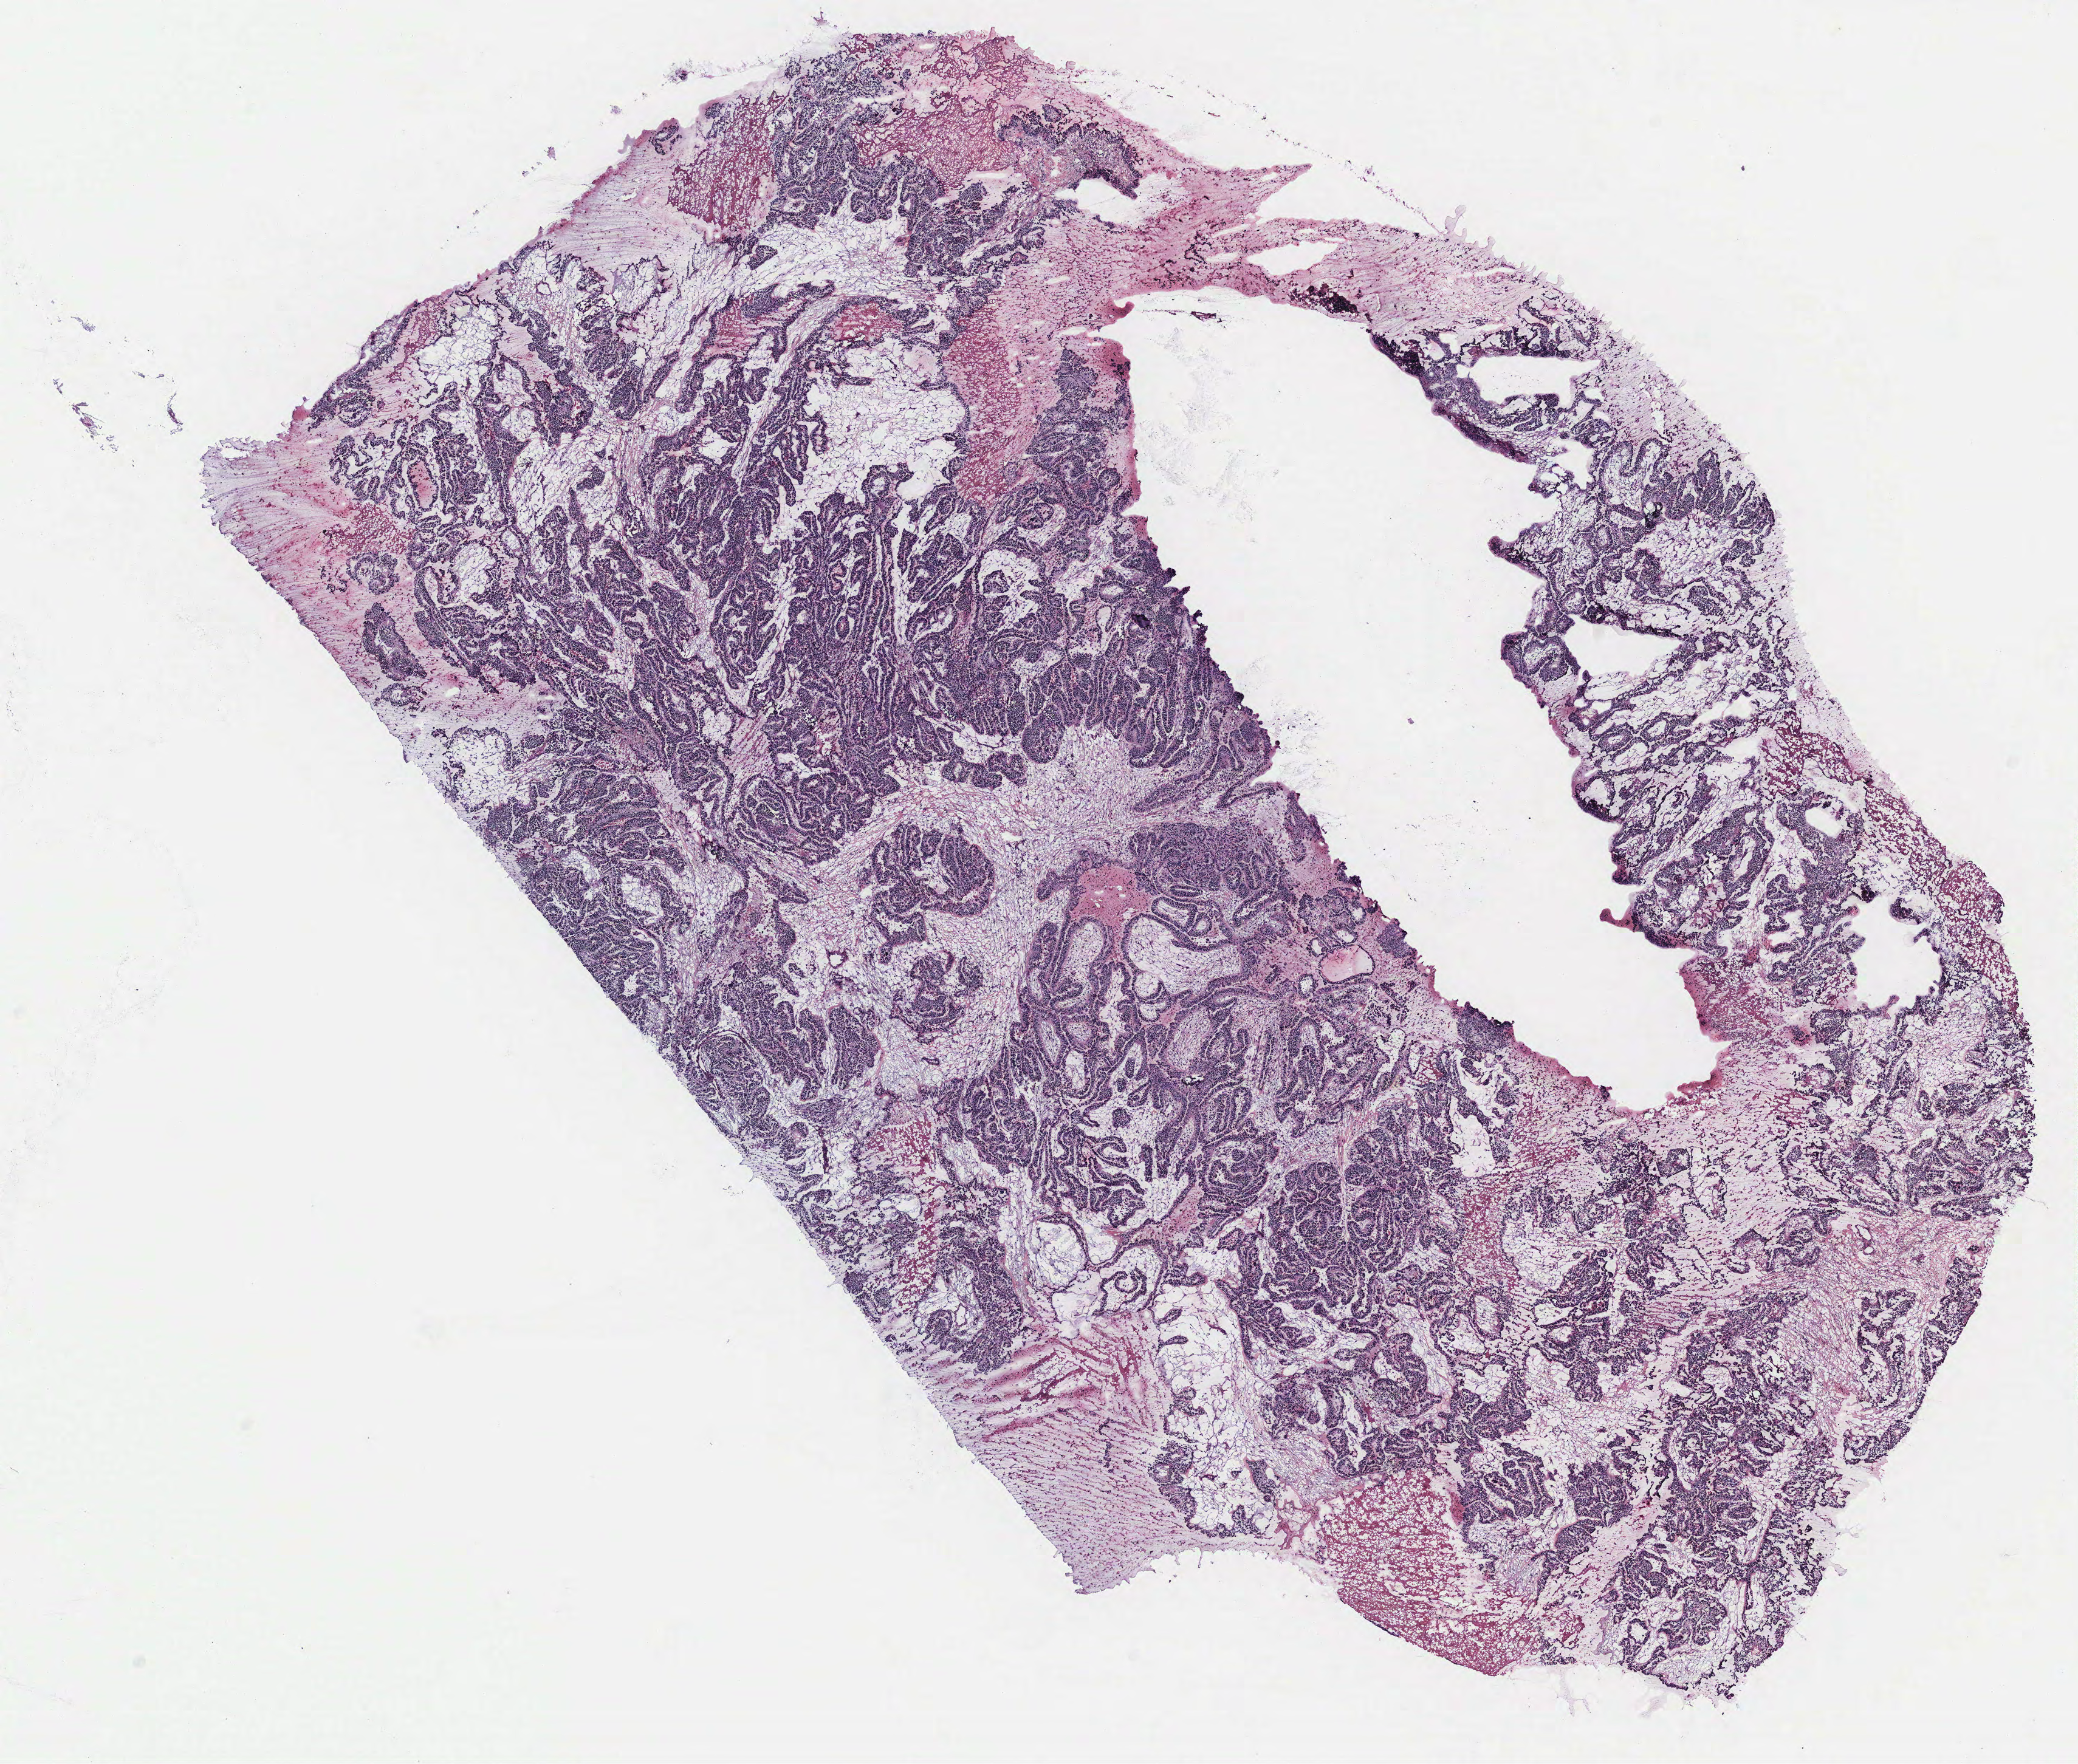
Whole-slide histology image, H&E — whole scanned area (about 13.7 x 11.6 mm, acquisition: 40x scan) shown as a low-resolution overview; tumour tissue sample, ovary. Female, 57 y/o.
Diagnosis: Serous adenocarcinoma, NOS. Primary tumour site (as recorded): ovary.